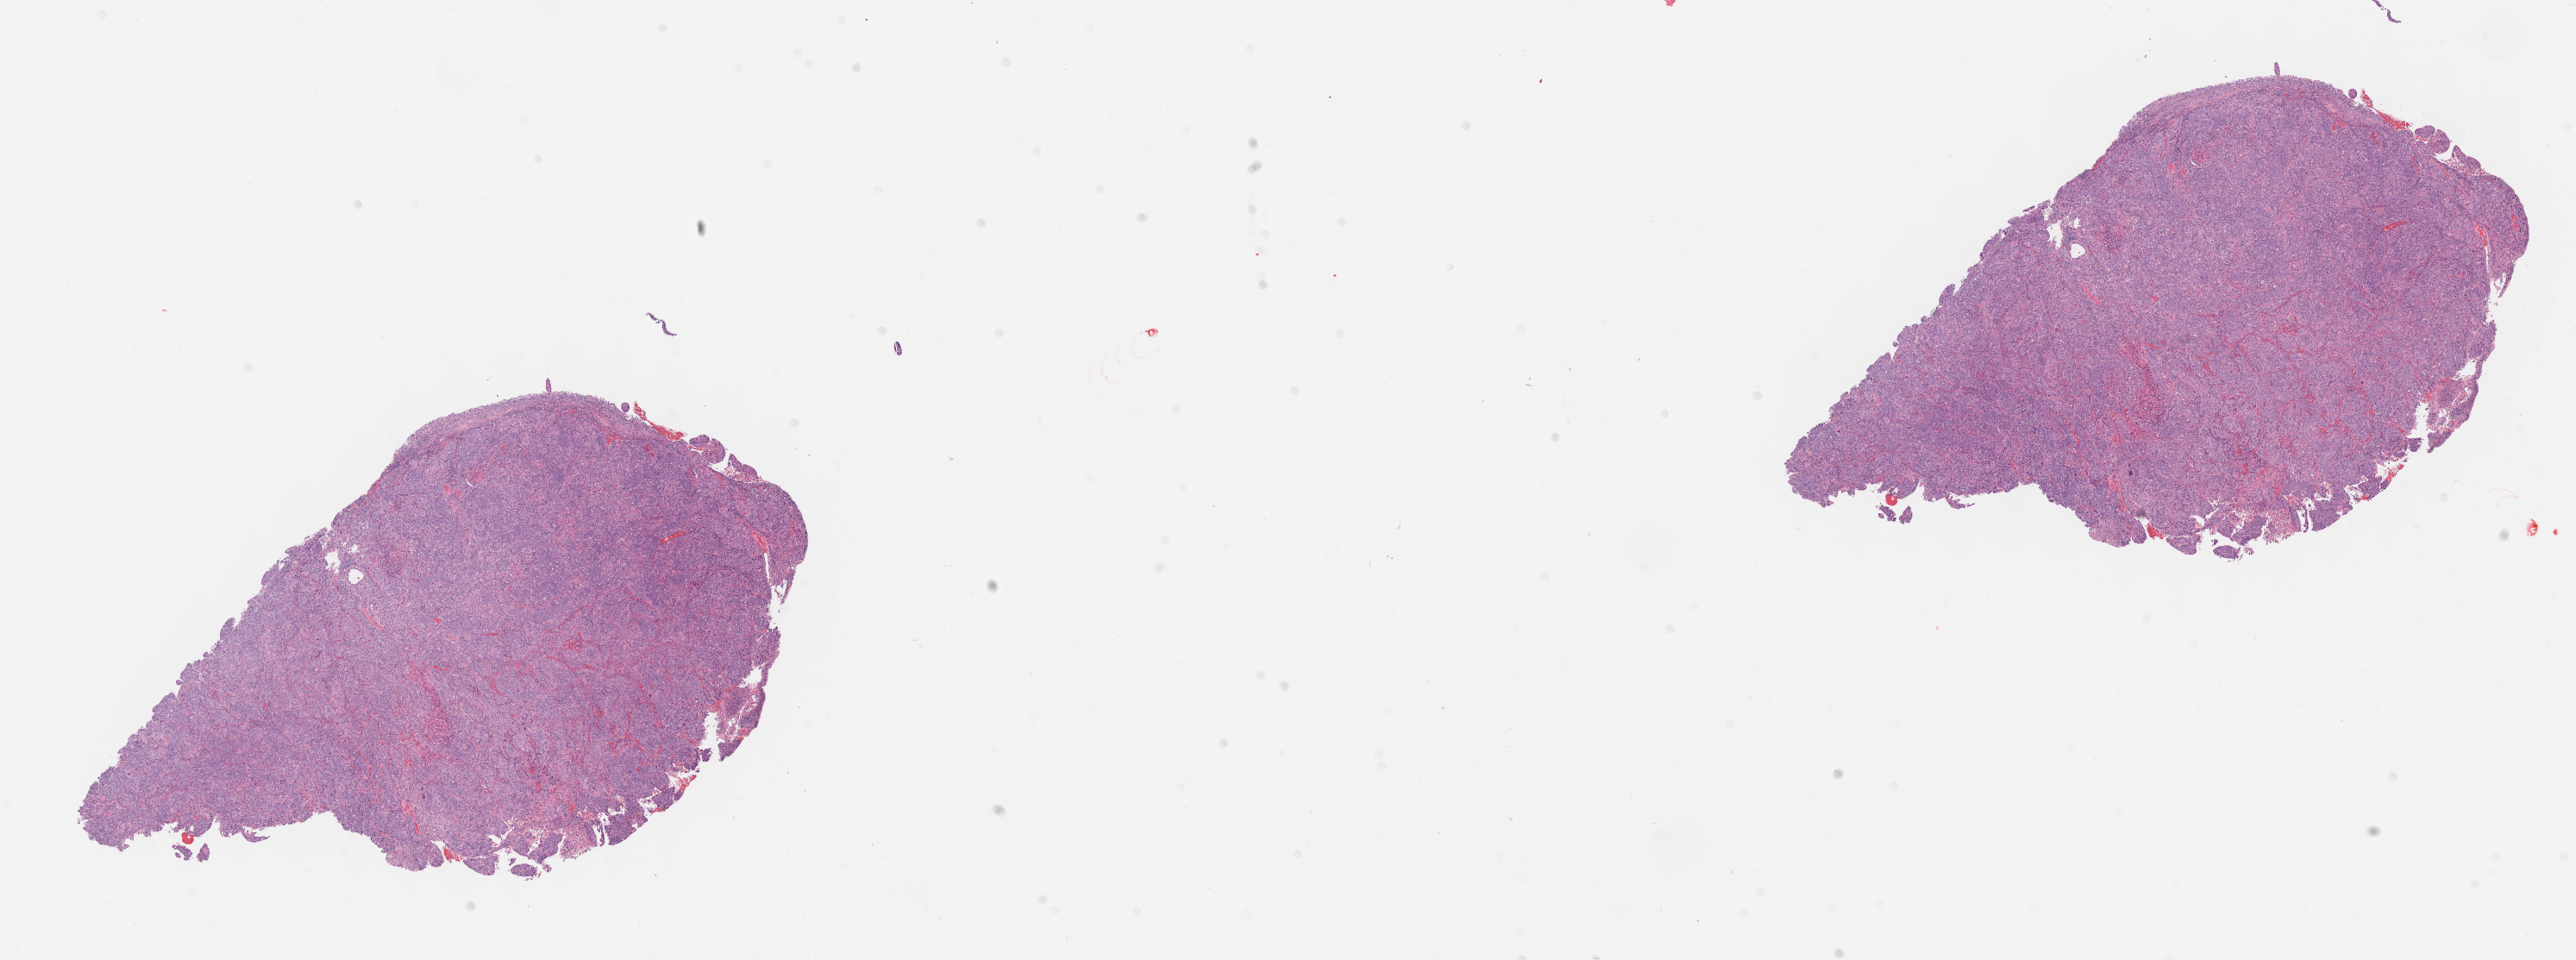
Whole-slide image, haematoxylin and eosin stain — low-resolution overview of the scanned area, about 24.2 x 9.0 mm, specimen: tumor tissue, anatomic site: cervix. Female patient, aged 68.
• diagnosis: Squamous cell carcinoma, large cell, nonkeratinizing, NOS